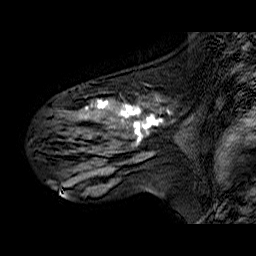
Breast MRI (dynamic contrast-enhanced), one sagittal slice; position 37 of 60 along the scan axis; dynamic contrast-enhanced series, time point 2 of 6 at this slice position (early post-contrast); 1.5 T; TE 6.3 ms, TR 32.9 ms; 4 mm slice thickness; 256 × 256 image matrix. Female patient. From the clinical record (not read from this slice): setting: breast cancer imaged before/during neoadjuvant chemotherapy; receptor status: HER2-positive.
Annotated regions visible in this slice (semi-automatic segmentation, software-assisted and operator-edited):
- analysis volume of interest (the breast-tissue region the enhancement analysis was run in; not a lesion): bounding box (x1, y1, x2, y2) in pixels: (32, 88, 174, 173)
- tumour enhancement mask (voxels above the 100 % enhancement threshold inside the analysis volume of interest): (85, 100, 163, 145)